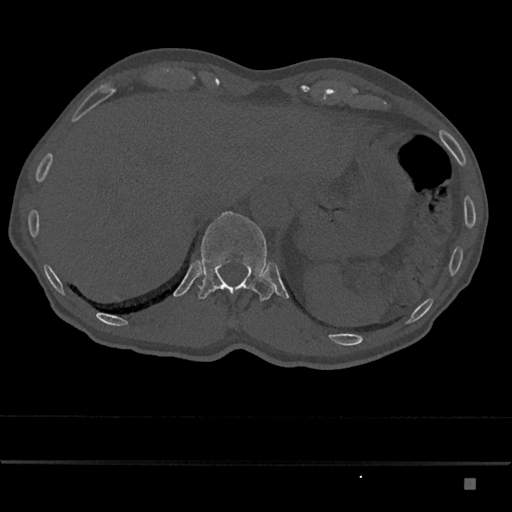
CT including the spine, one axial slice; reconstruction kernel Br40s/3; 120 kVp; bone window (W 1800 / L 400 HU); 0.5 mm slice thickness; 512 × 512 image matrix, field of view 390 × 390 mm. Patient: male, 72 years. Case-level facts recorded for this patient, not image findings: primary cancer: prostate.
Annotated regions visible in this slice (semi-automatically segmented with operator editing):
- T12 vertebra: bounding box (x1, y1, x2, y2) in pixels: (198, 211, 276, 301)